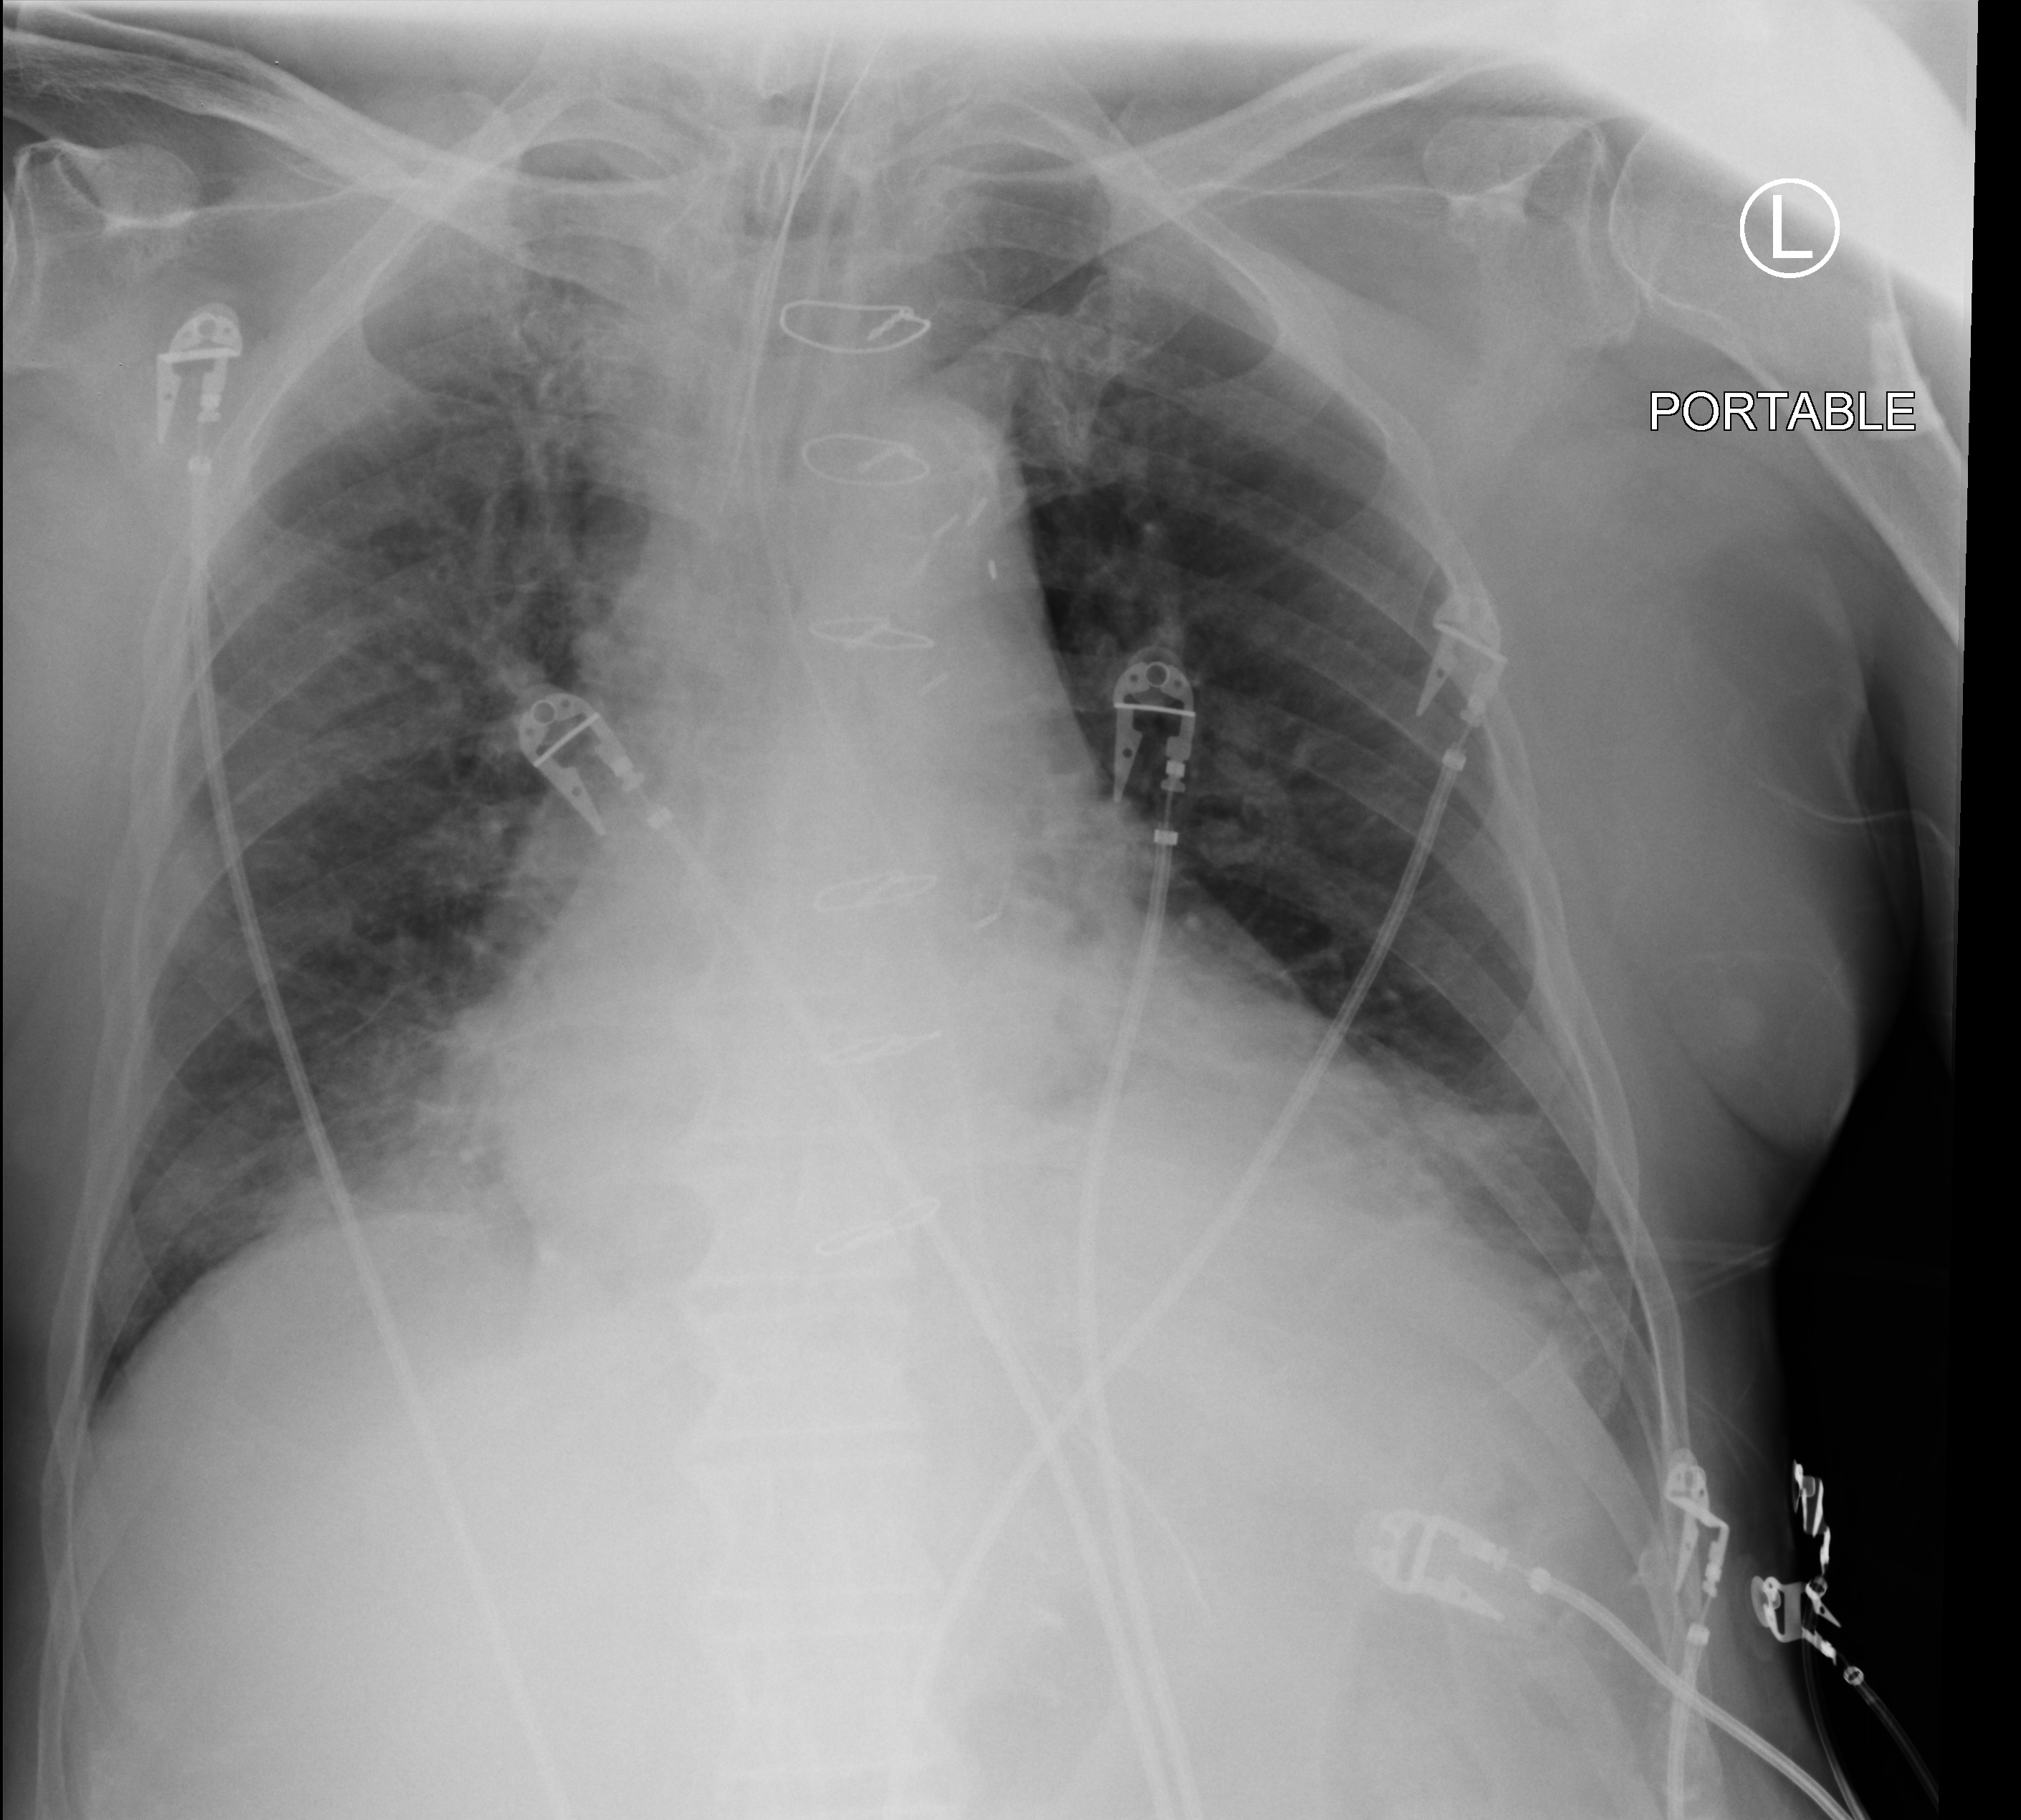
Bedside chest radiograph (computed radiography), anteroposterior (AP) projection. Male patient hospitalised with COVID-19, age 75–90 years.
From the hospital-stay record, not from the radiograph (when in the stay this image was taken is not recorded): hypertension (admission record): yes.